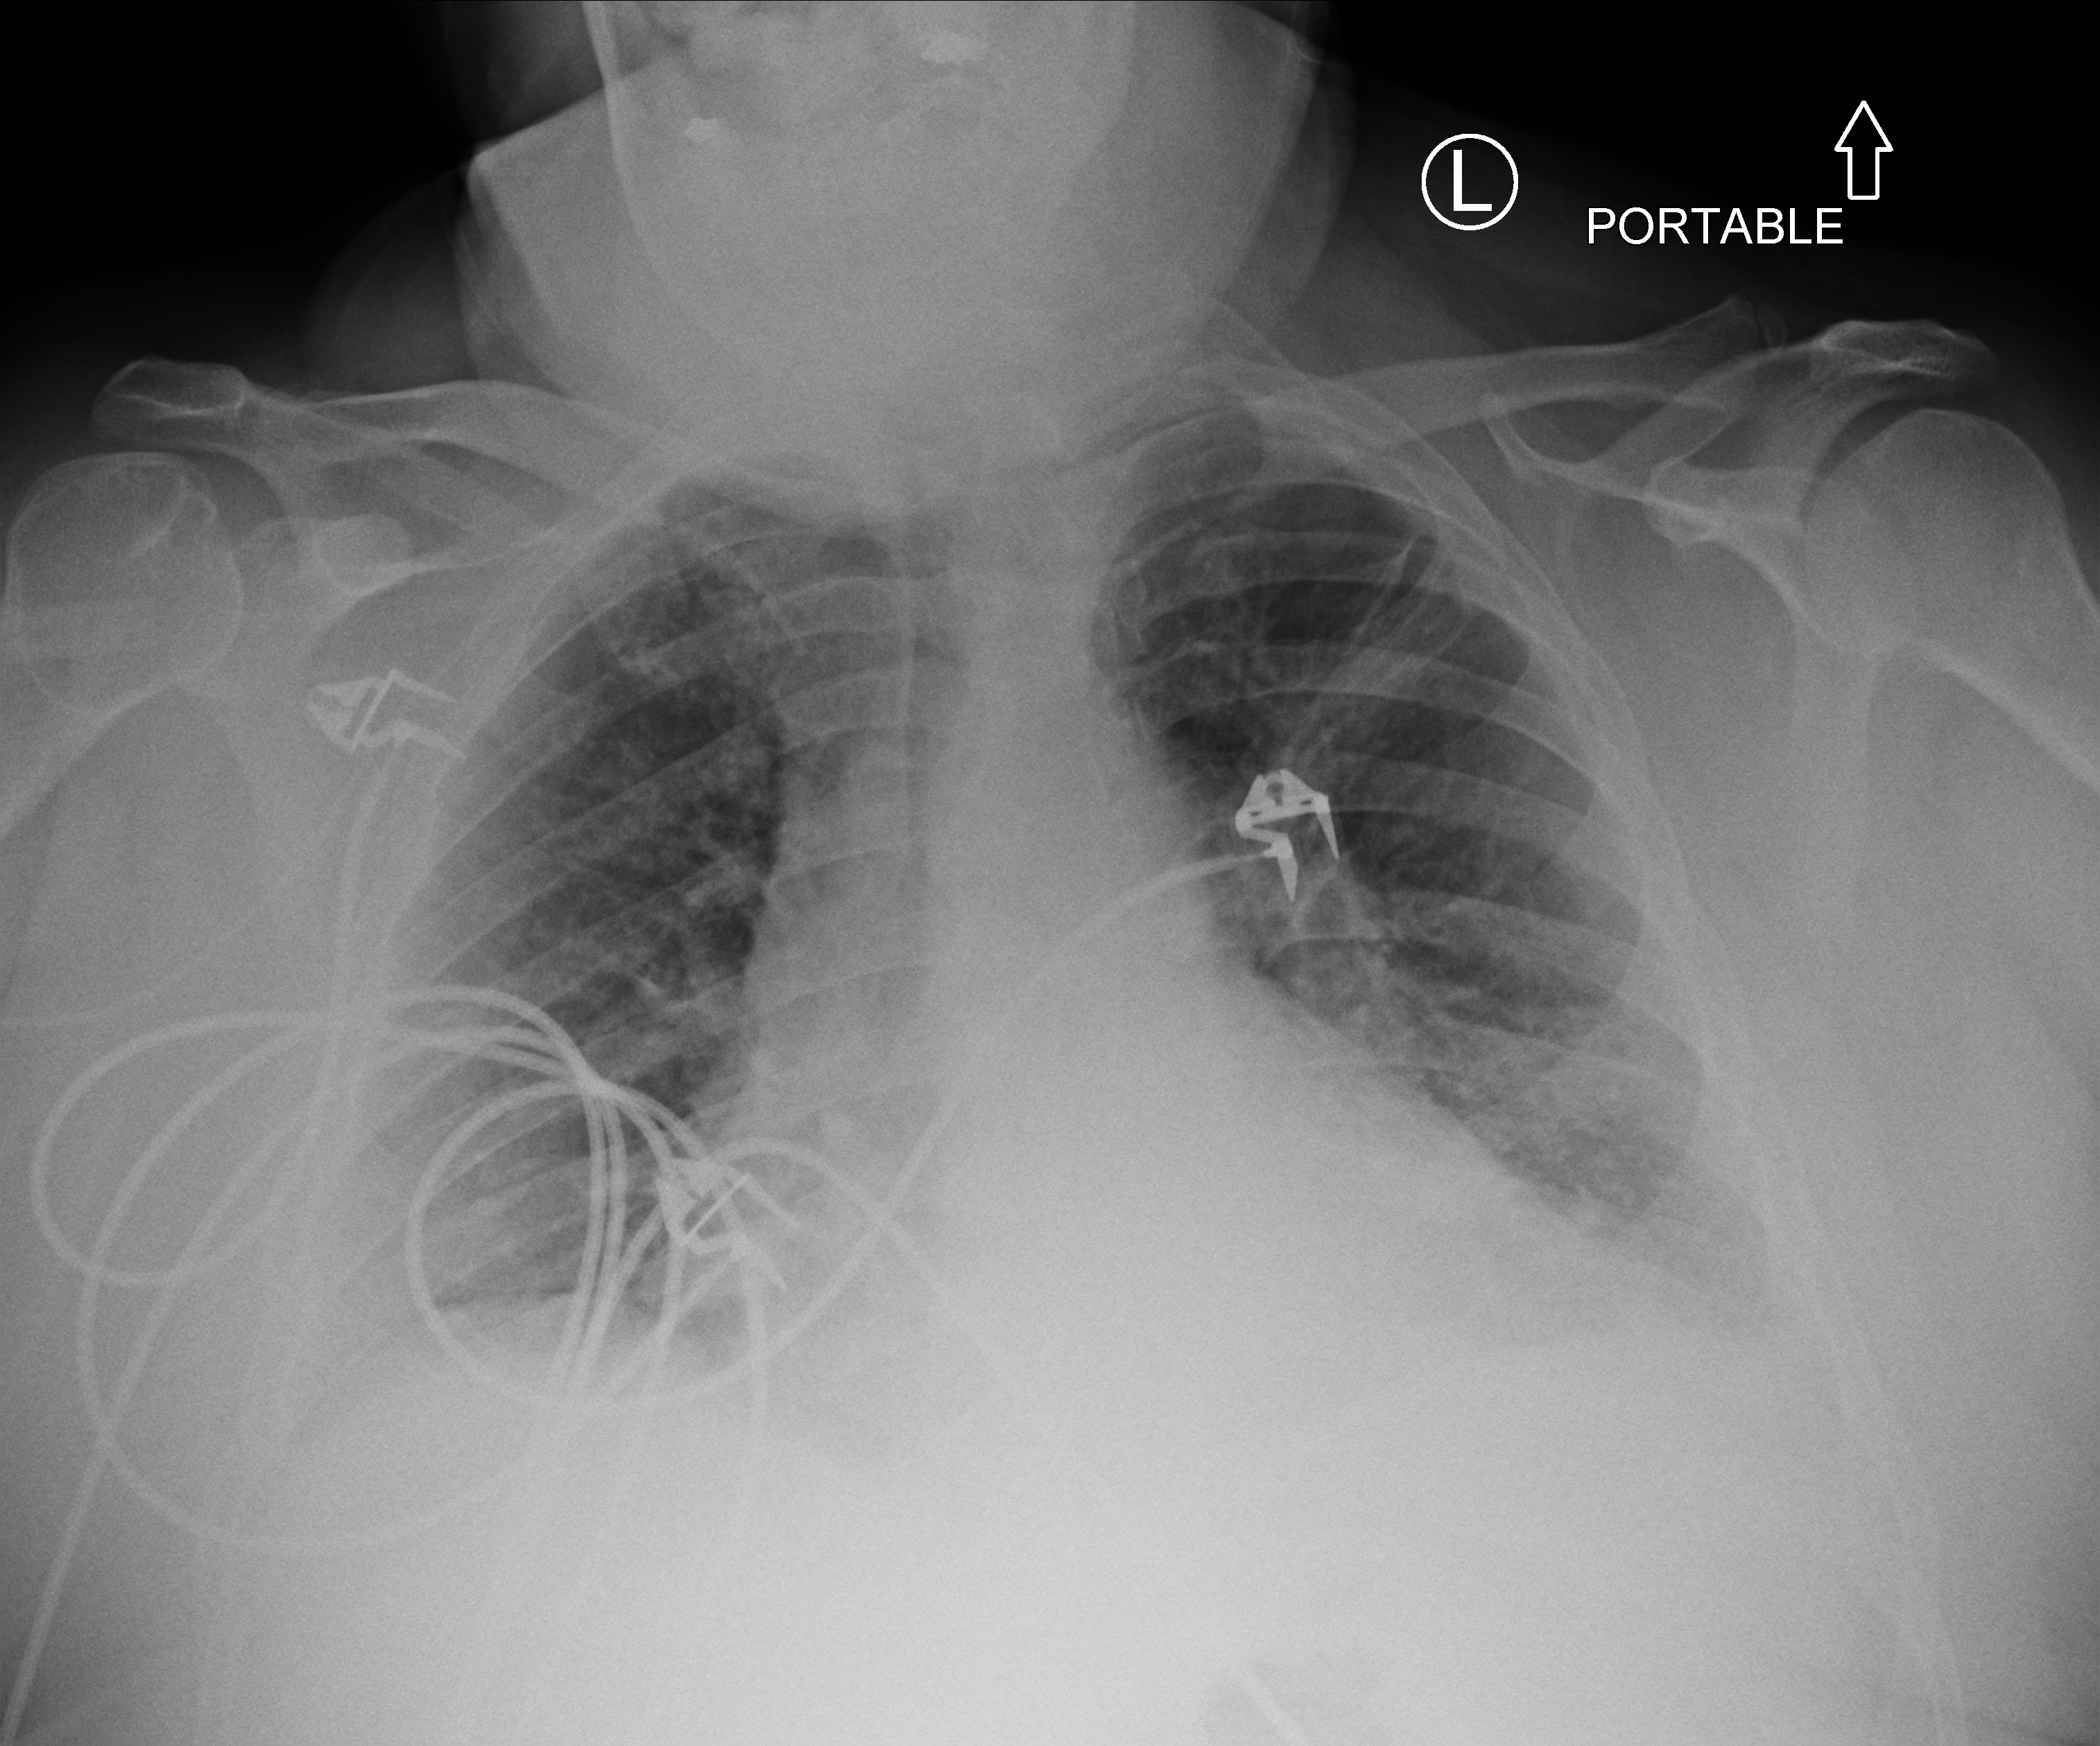
Bedside chest radiograph (computed radiography). Patient hospitalised with COVID-19; male, aged 60–74 years.
Hospital-stay facts (about this admission, not read from this image; timing relative to this image not recorded): COPD (admission record): no; mechanically ventilated during this hospital stay: no.